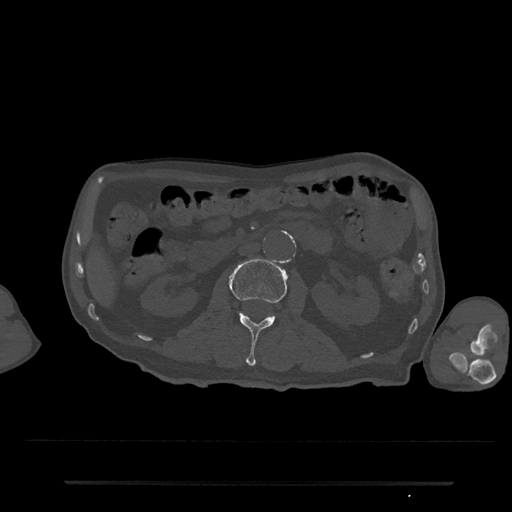
CT including the spine, one axial slice; reconstruction kernel Br40s/3; 120 kVp; bone window (W 1800 / L 400 HU); 512 × 512 image matrix, field of view 427 × 427 mm. Male patient, age 74 years. Case-level facts recorded for this patient, not image findings: primary cancer: prostate.
Outlined on this slice (semi-automatic segmentation, software-assisted and operator-edited):
- L2 vertebra: box from (x=230, y=258) to (x=287, y=366) px